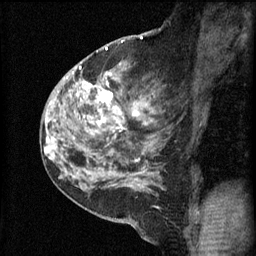
Breast MRI (dynamic contrast-enhanced), one sagittal slice. Position 36 of 60 along the scan axis. 3 images stored at this slice position (order not interpretable as contrast timing). 1.5 T. TE 4.2 ms, TR 11 ms. 2.3 mm slice thickness. 256 × 256 image matrix, field of view 180 × 180 mm. Female patient, age 52 years.
Outlined on this slice (semi-automatically segmented with operator editing):
- analysis volume of interest (the breast-tissue region the enhancement analysis was run in; not a lesion): bounding box [x1, y1, x2, y2] px = [86, 76, 161, 157]
- tumour enhancement mask (voxels above the 70 % enhancement threshold inside the analysis volume of interest): [96, 84, 139, 131]